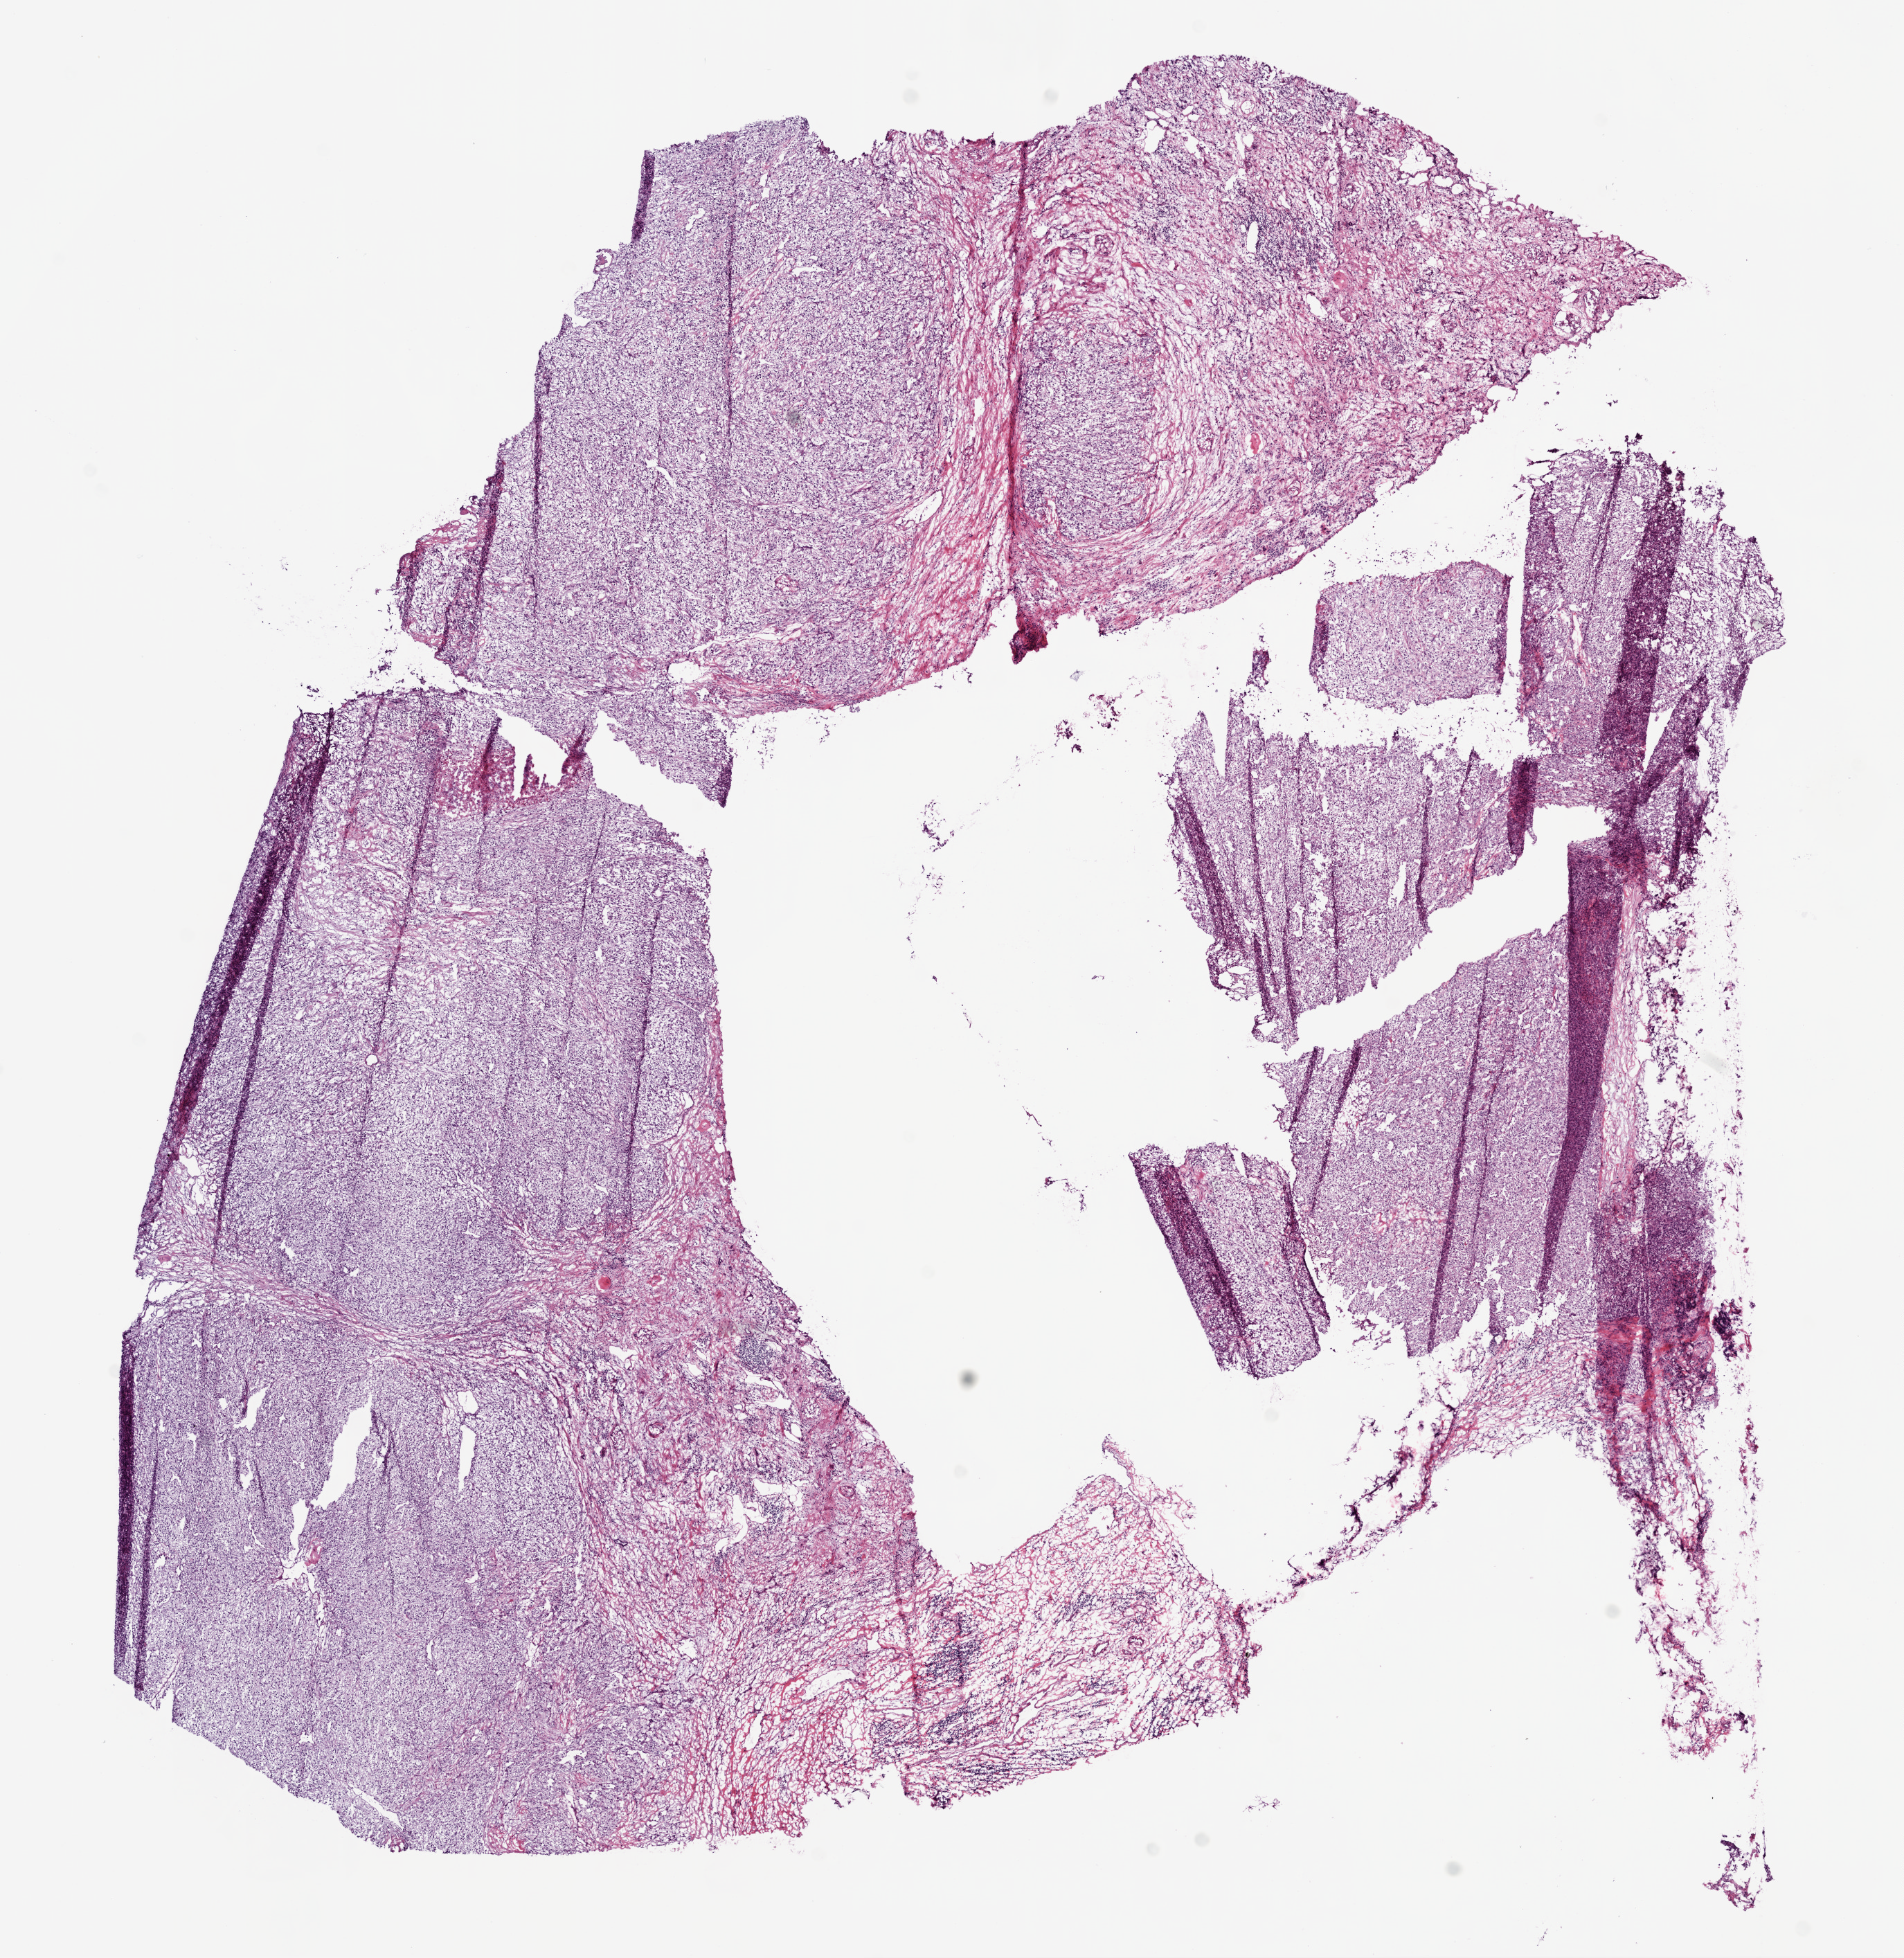
Digitized Hematoxylin and eosin (H&E) stained tissue section (whole slide) — low-resolution overview of the scanned area, about 11.0 x 11.3 mm, frozen section from the bottom of the tissue portion, primary tumour sample from the kidney. Female, age 76 years at initial diagnosis. Histologic grade: G2 (moderately differentiated). Composition of this section per pathologist review: tumour cells 85%, tumour nuclei 75%, normal cells 0%, stromal cells 15%, necrosis 0%.
AJCC pathologic stage: III. Histologic diagnosis: Clear cell adenocarcinoma, NOS.